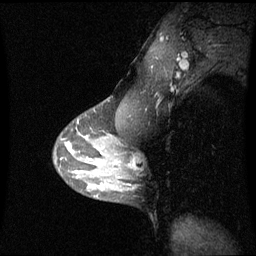
Breast MRI (dynamic contrast-enhanced), one sagittal slice; slice 46 of 60 in the series (ordered by position); dynamic contrast-enhanced series, image 2 of 3 at this slice position (ordered by acquisition); 1.5 T; TE 4.2 ms, TR 8.9 ms; 2 mm slice thickness; 256 × 256 image matrix, field of view 230 × 230 mm. Female patient, age 42 years. From the clinical record (not read from this slice): setting: breast cancer imaged before/during neoadjuvant chemotherapy; receptor status: triple-negative.
Annotated regions visible in this slice (semi-automatic segmentation, software-assisted and operator-edited):
- analysis volume of interest (the breast-tissue region the enhancement analysis was run in; not a lesion): box from (x=114, y=150) to (x=134, y=180) px
- tumour enhancement mask (voxels above the 70 % enhancement threshold inside the analysis volume of interest): (x=128, y=163)–(x=131, y=167)